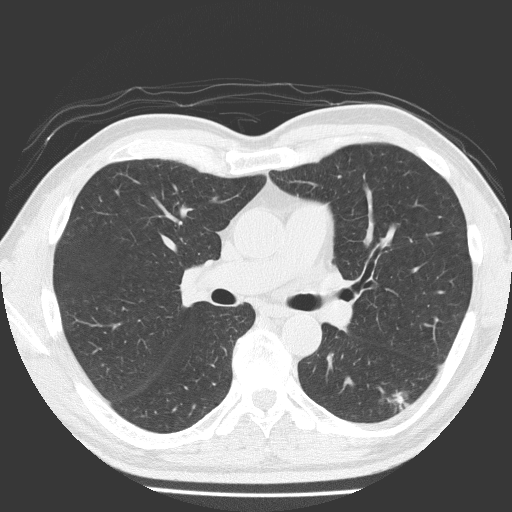
Low-dose screening chest CT, one axial slice. Slice 107 of 184 in the series (ordered by position). 120 kVp. Lung window (W 1500 / L -600 HU). 2 mm slice thickness. 512 × 512 image matrix, field of view 348 × 348 mm.
Structures marked on this image (expert manual segmentation):
- lesion 1 (tumor, lower lobe of left lung): bounding box (x1, y1, x2, y2) in pixels: (380, 389, 409, 410)